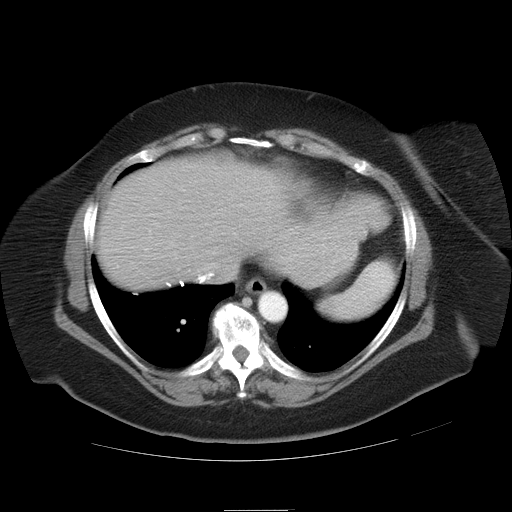
Contrast-enhanced abdominal CT, one axial slice. Position 32 of 37 along the scan axis. Intravenous contrast given. Soft-tissue window (W 400 / L 40 HU). 512 × 512 image matrix, field of view 422 × 422 mm. Female patient, age 68 years. From the clinical record (not read from this slice): diagnosis: colorectal cancer liver metastases, imaged before liver resection; multiple liver metastases: no; largest metastasis: 2 cm; disease in both lobes: no.
Annotated regions visible in this slice (expert manual segmentation):
- liver: bounding box [x1, y1, x2, y2] px = [98, 156, 388, 292]
- planned liver remnant (the part of the liver to remain after resection): [98, 156, 388, 292]